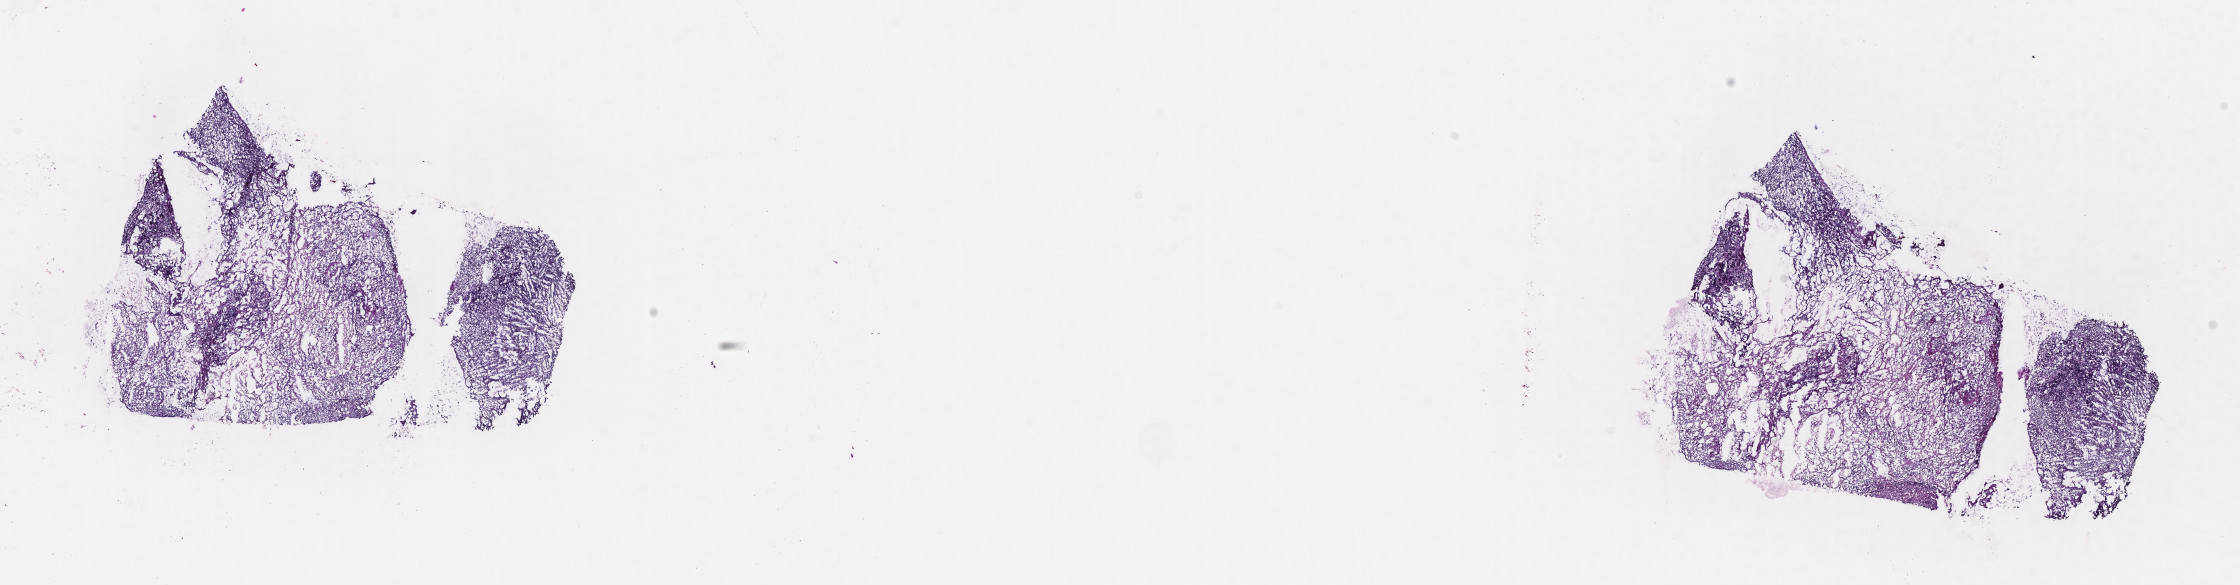
Whole-slide image, H&E stain, a low-resolution overview of the entire scanned area, about 18.1 x 4.7 mm. Frozen section. Primary tumor. Site: soft tissue of abdomen. Female patient; age at initial diagnosis 8 years. Slide review estimates, as recorded: tumor cells 40%, tumor nuclei 65%, stromal cells 40%, necrosis 15%, normal cells 5%. Inflammatory infiltration, as recorded: lymphocyte infiltration 50%, monocyte infiltration 20%, neutrophil infiltration 5%.
- Ann Arbor stage (patient): Stage IV
- histologic diagnosis: Burkitt lymphoma, NOS